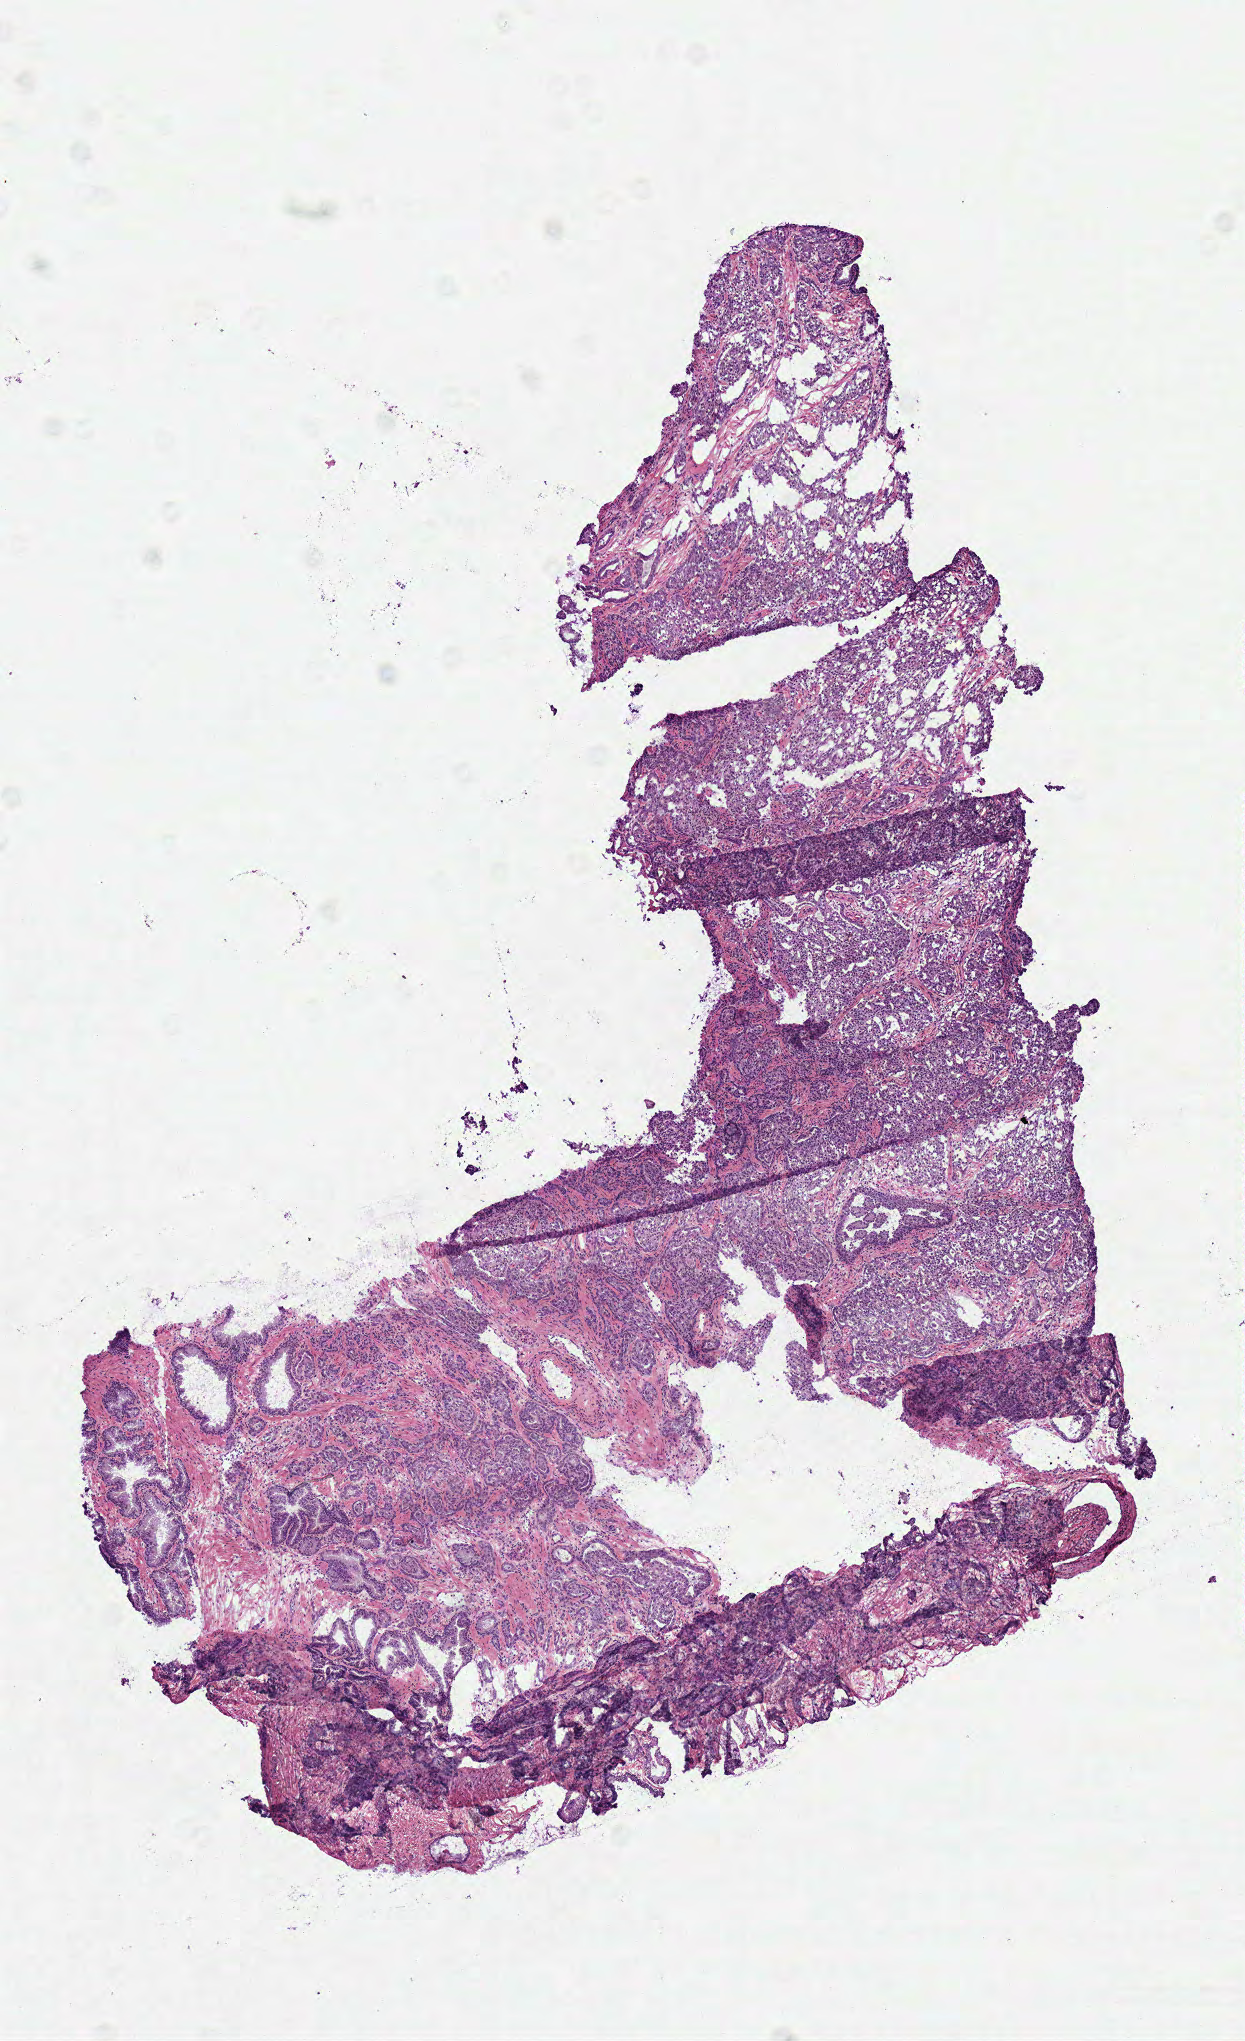
Whole-slide histology image, Hematoxylin and eosin (H&E) stained, low-resolution overview of the scanned area, about 4.9 x 8.0 mm (acquisition: 40x scan); frozen section from the top of the tissue portion; prostate, primary tumour sample. Male patient; age at initial diagnosis 66 years. Gleason score: 7 (4+3). Pathologist review of this section (percent, as recorded): tumour cells 75%, tumour nuclei 80%, normal cells 10%, stromal cells 15%, necrosis 0%. Infiltration values recorded for this section: lymphocyte infiltration 1%, monocyte infiltration 0%, neutrophil infiltration 0%.
Lymph nodes positive (case pathology): 0 of 13 examined. Laterality: bilateral. Pathologic diagnosis: Acinar cell carcinoma (prostate gland).